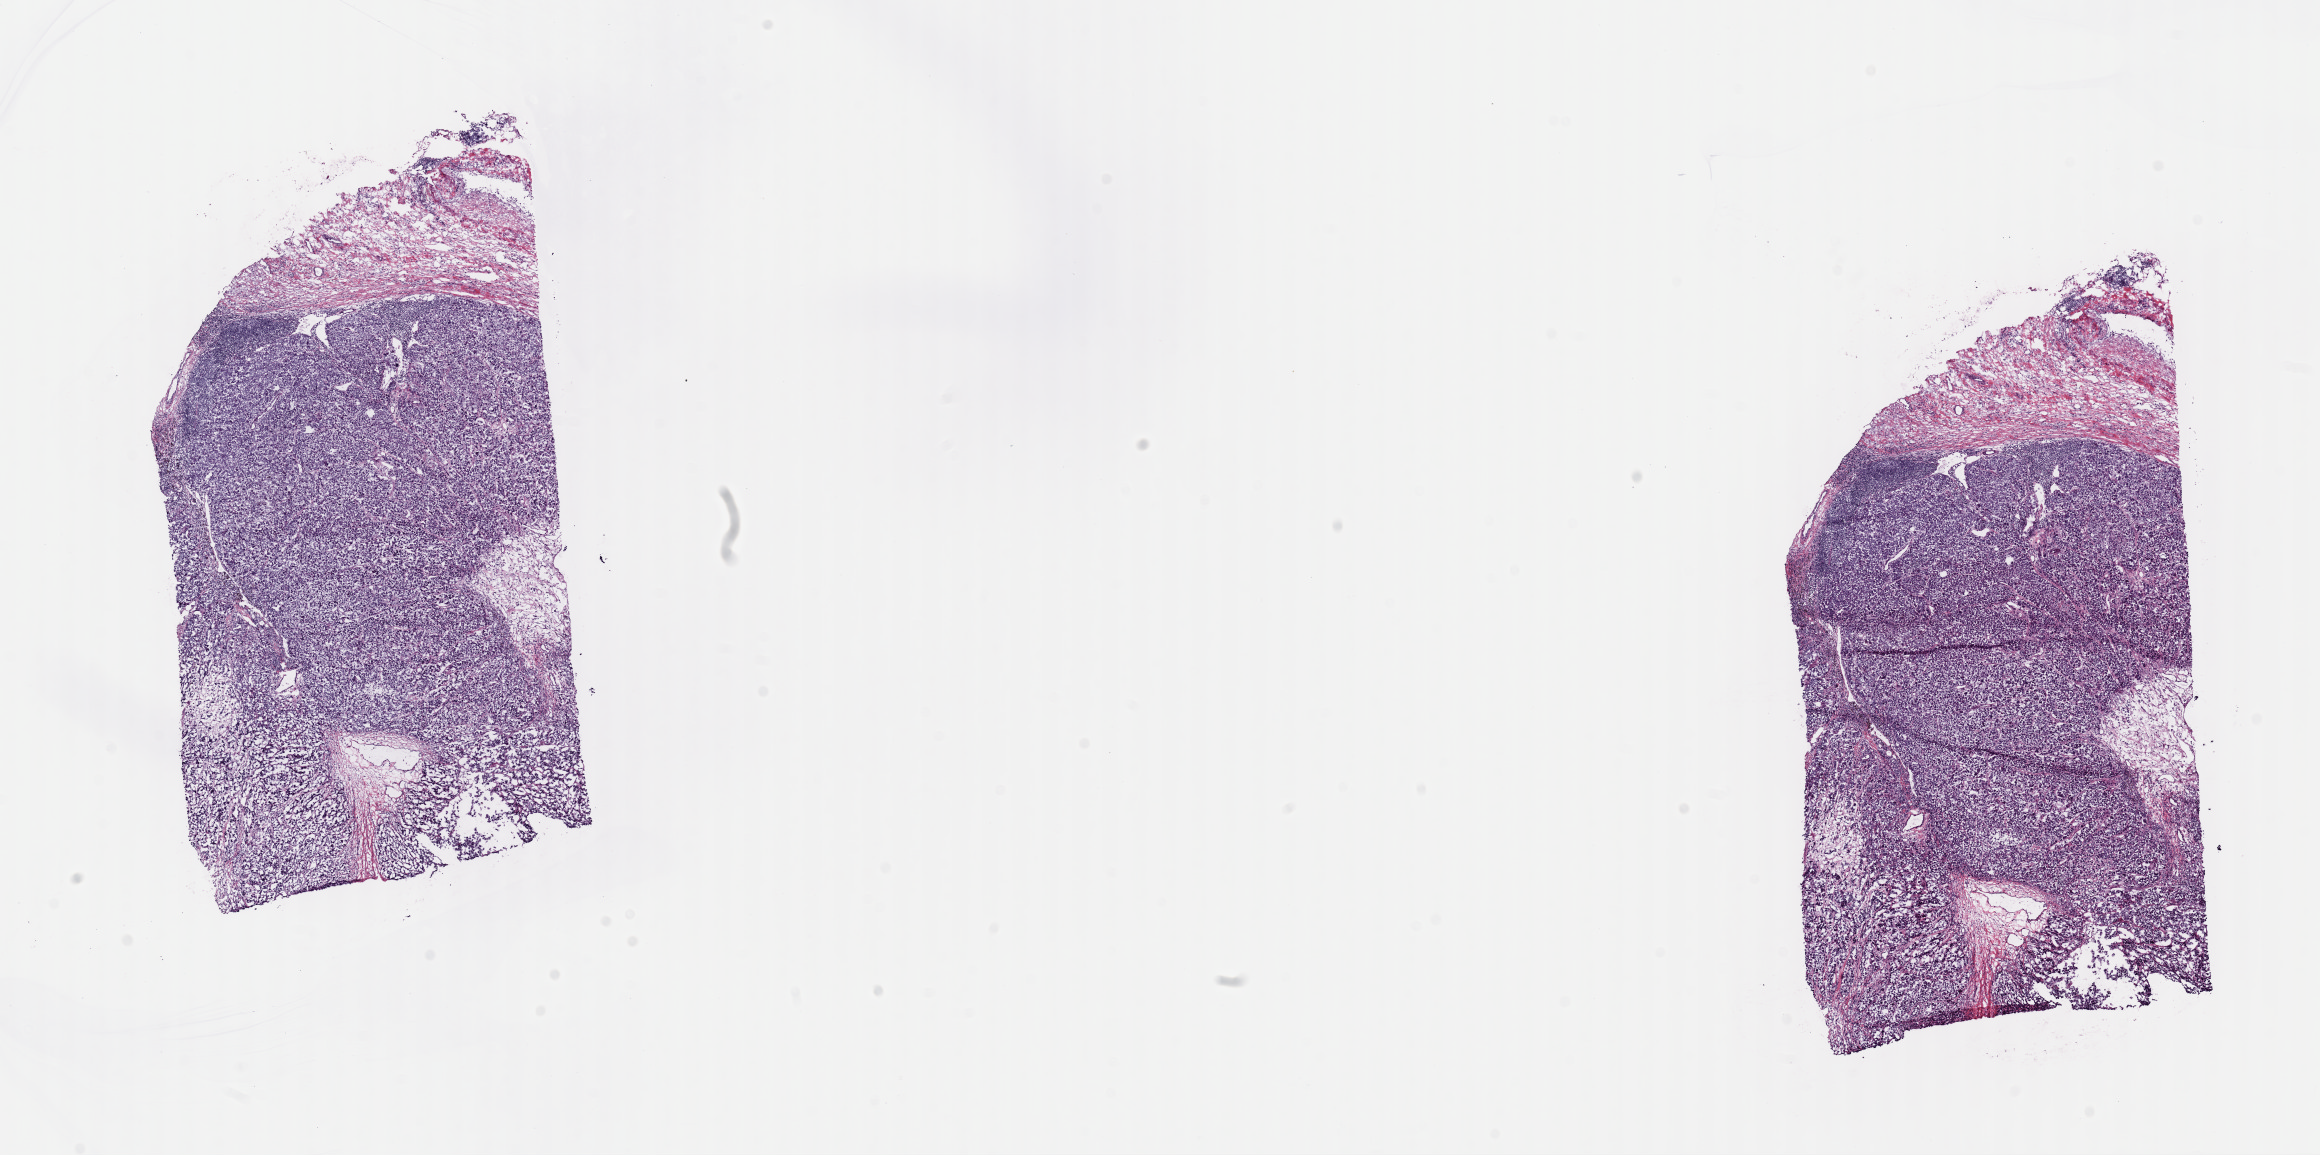
H&E whole-slide image, whole scanned area (about 18.3 x 9.1 mm) shown as a low-resolution overview. Frozen section from the top of the tissue portion. Metastatic tumour sample, sampled site not recorded. Female patient; age at initial diagnosis 59 years. Composition of this section per pathologist review: tumour cells 80%, tumour nuclei 80%, normal cells 0%, stromal cells 20%, necrosis 0%. Infiltration values recorded for this section: lymphocyte infiltration 2%, monocyte infiltration 2%, neutrophil infiltration 0%.
This section: metastatic tumour tissue. Patient diagnosis: Malignant melanoma, NOS.